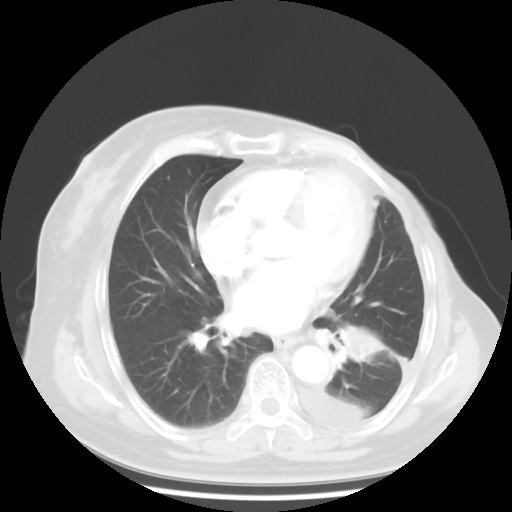
Chest CT, one axial slice; slice 20 of 48 in the series (ordered by position); reconstruction kernel STANDARD; lung window (W 1500 / L -600 HU); 5 mm slice thickness; 512 × 512 image matrix, field of view 360 × 360 mm. Female patient, age 63 years. From the clinical record (not read from this slice): clinical TNM (as recorded): T2 N0 M1.
Outlined on this slice (bounding box drawn by a radiologist):
- lung tumour (recorded histology: adenocarcinoma): bounding box <334,318,393,371> (left, top, right, bottom; pixels)